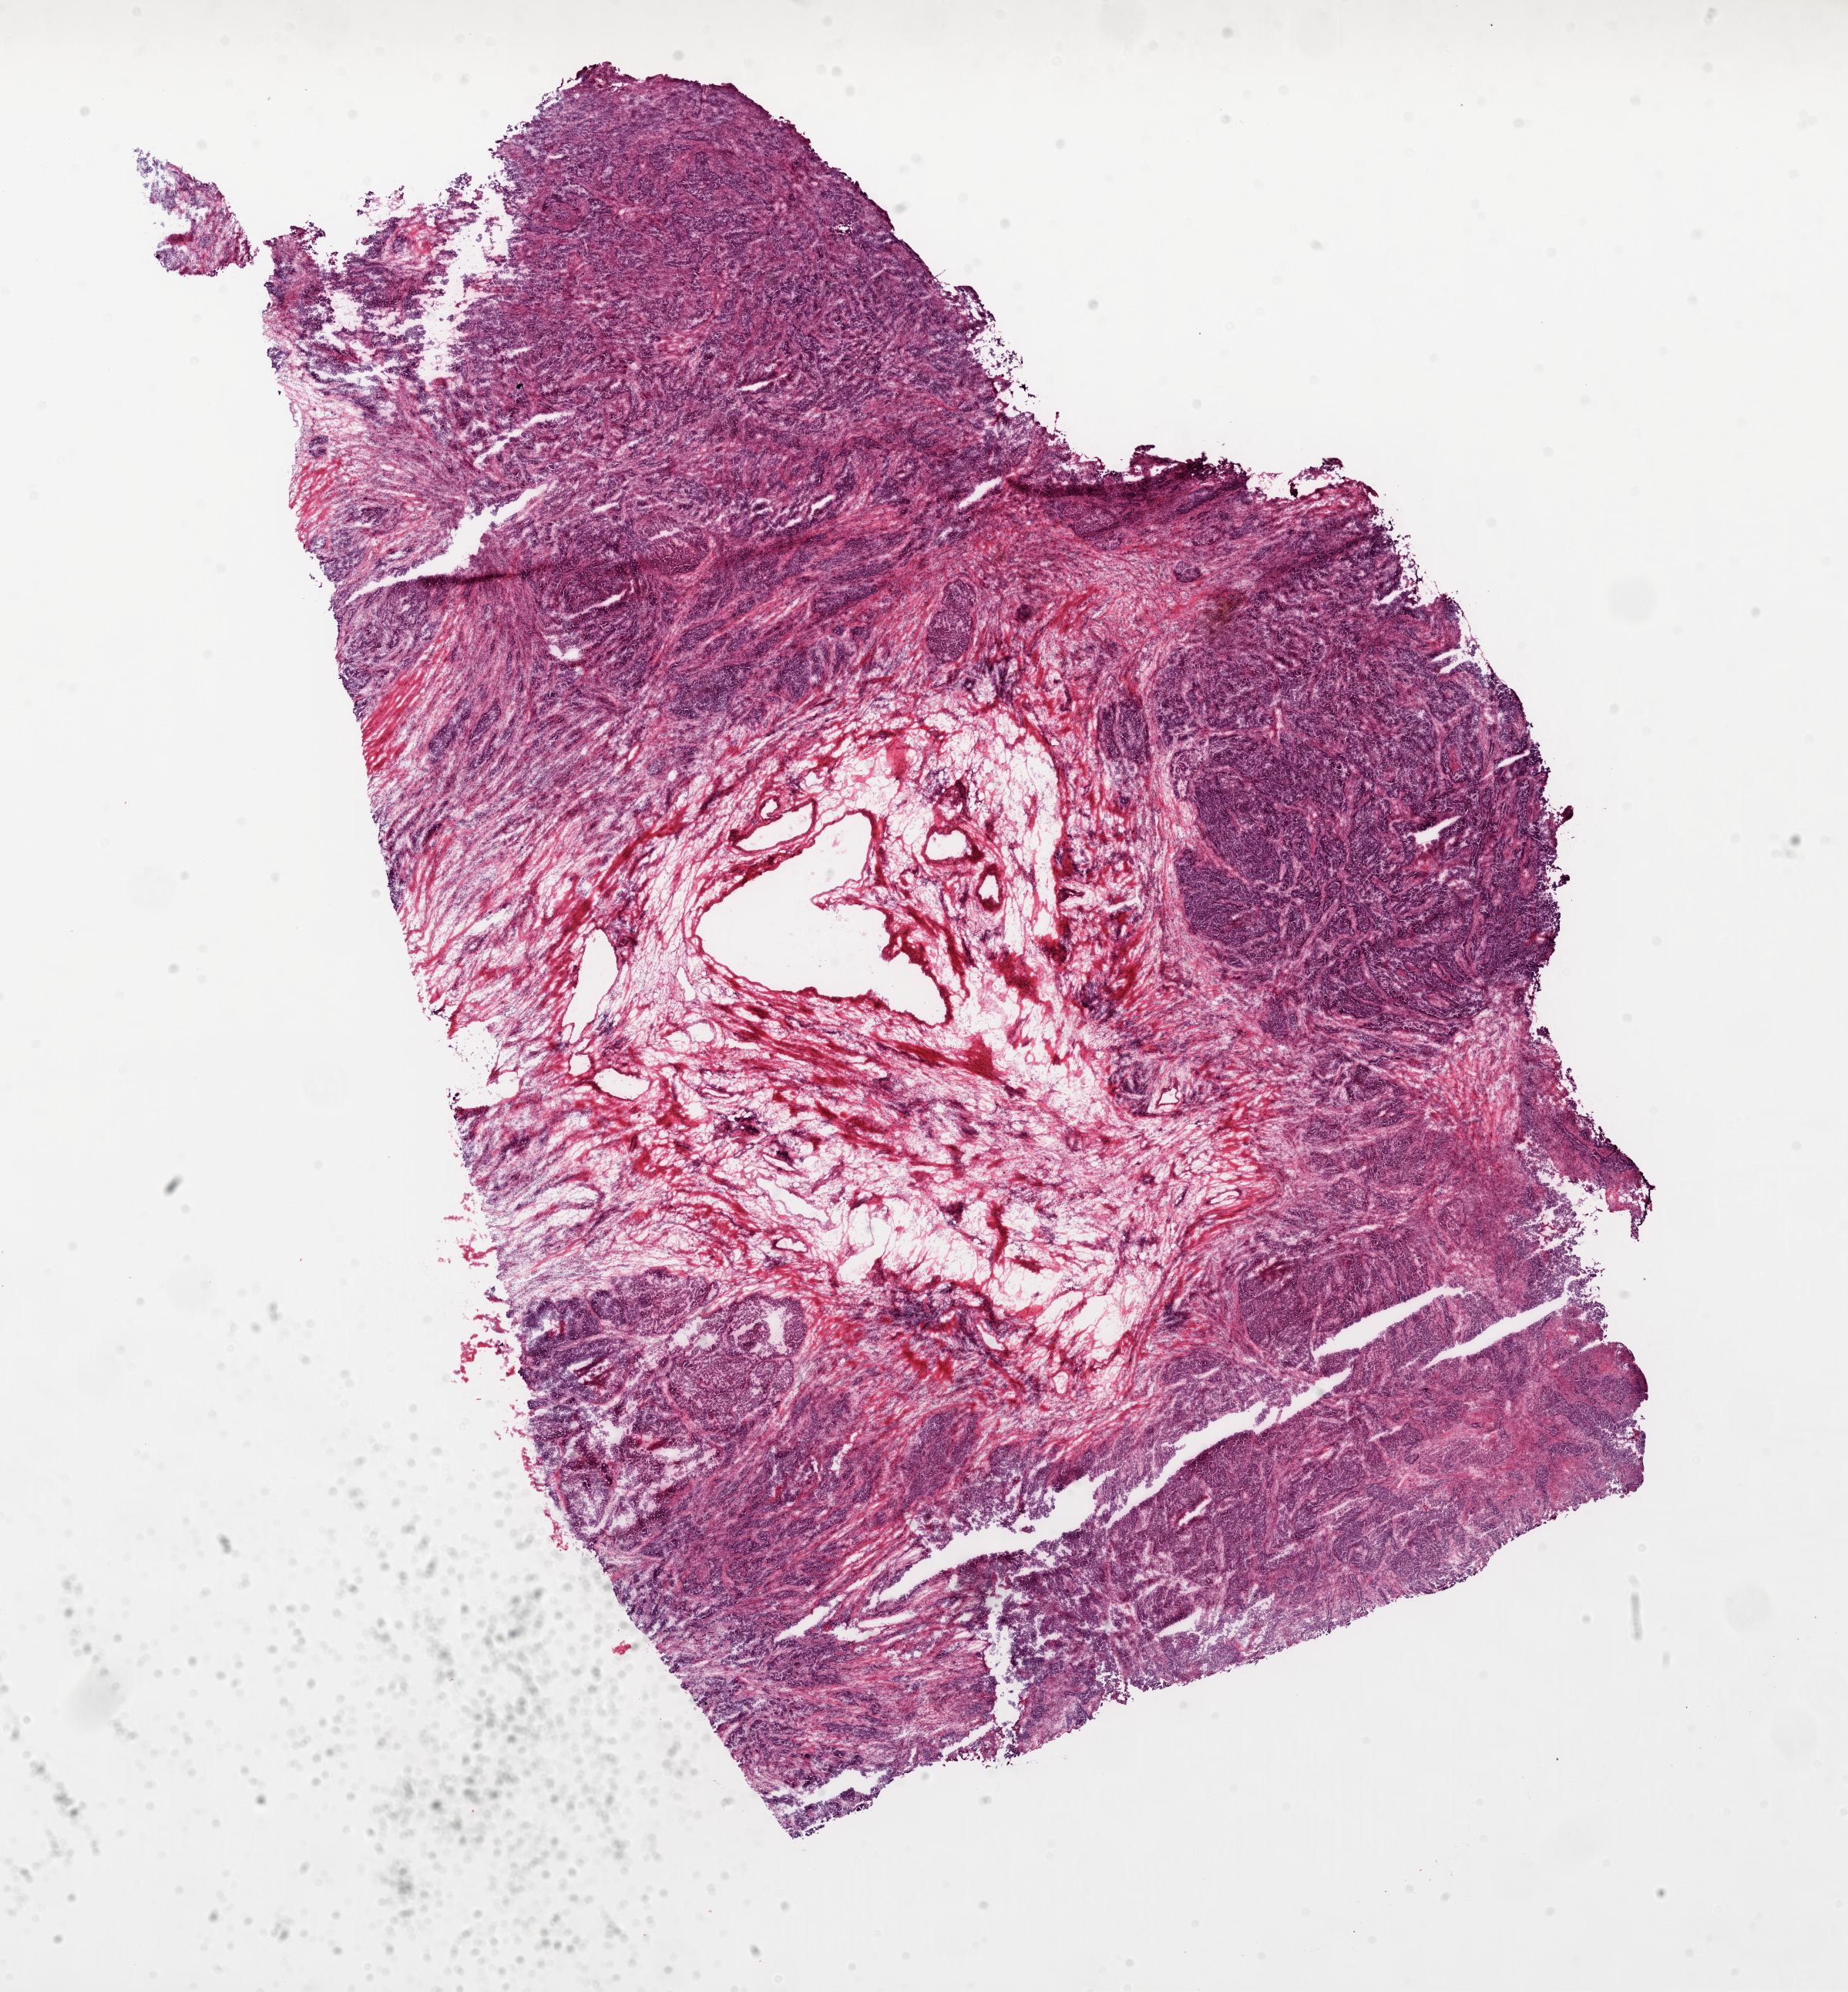
Digitized Hematoxylin and eosin (H&E) stained tissue section (whole slide) — shown as a low-resolution overview of the whole scanned area (about 19.3 x 20.8 mm), frozen section from the top of the tissue portion, primary tumour sample from the ovary. Female patient; age at initial diagnosis 55 years. Histologic grade: G3 (poorly differentiated). Slide review estimates, as recorded: tumour cells 75%, tumour nuclei 85%, normal cells 0%, stromal cells 20%, necrosis 5%. Inflammatory infiltration, as recorded: lymphocyte infiltration 100%.
- FIGO stage: IV
- laterality: bilateral
- pathologic diagnosis: Serous cystadenocarcinoma, NOS